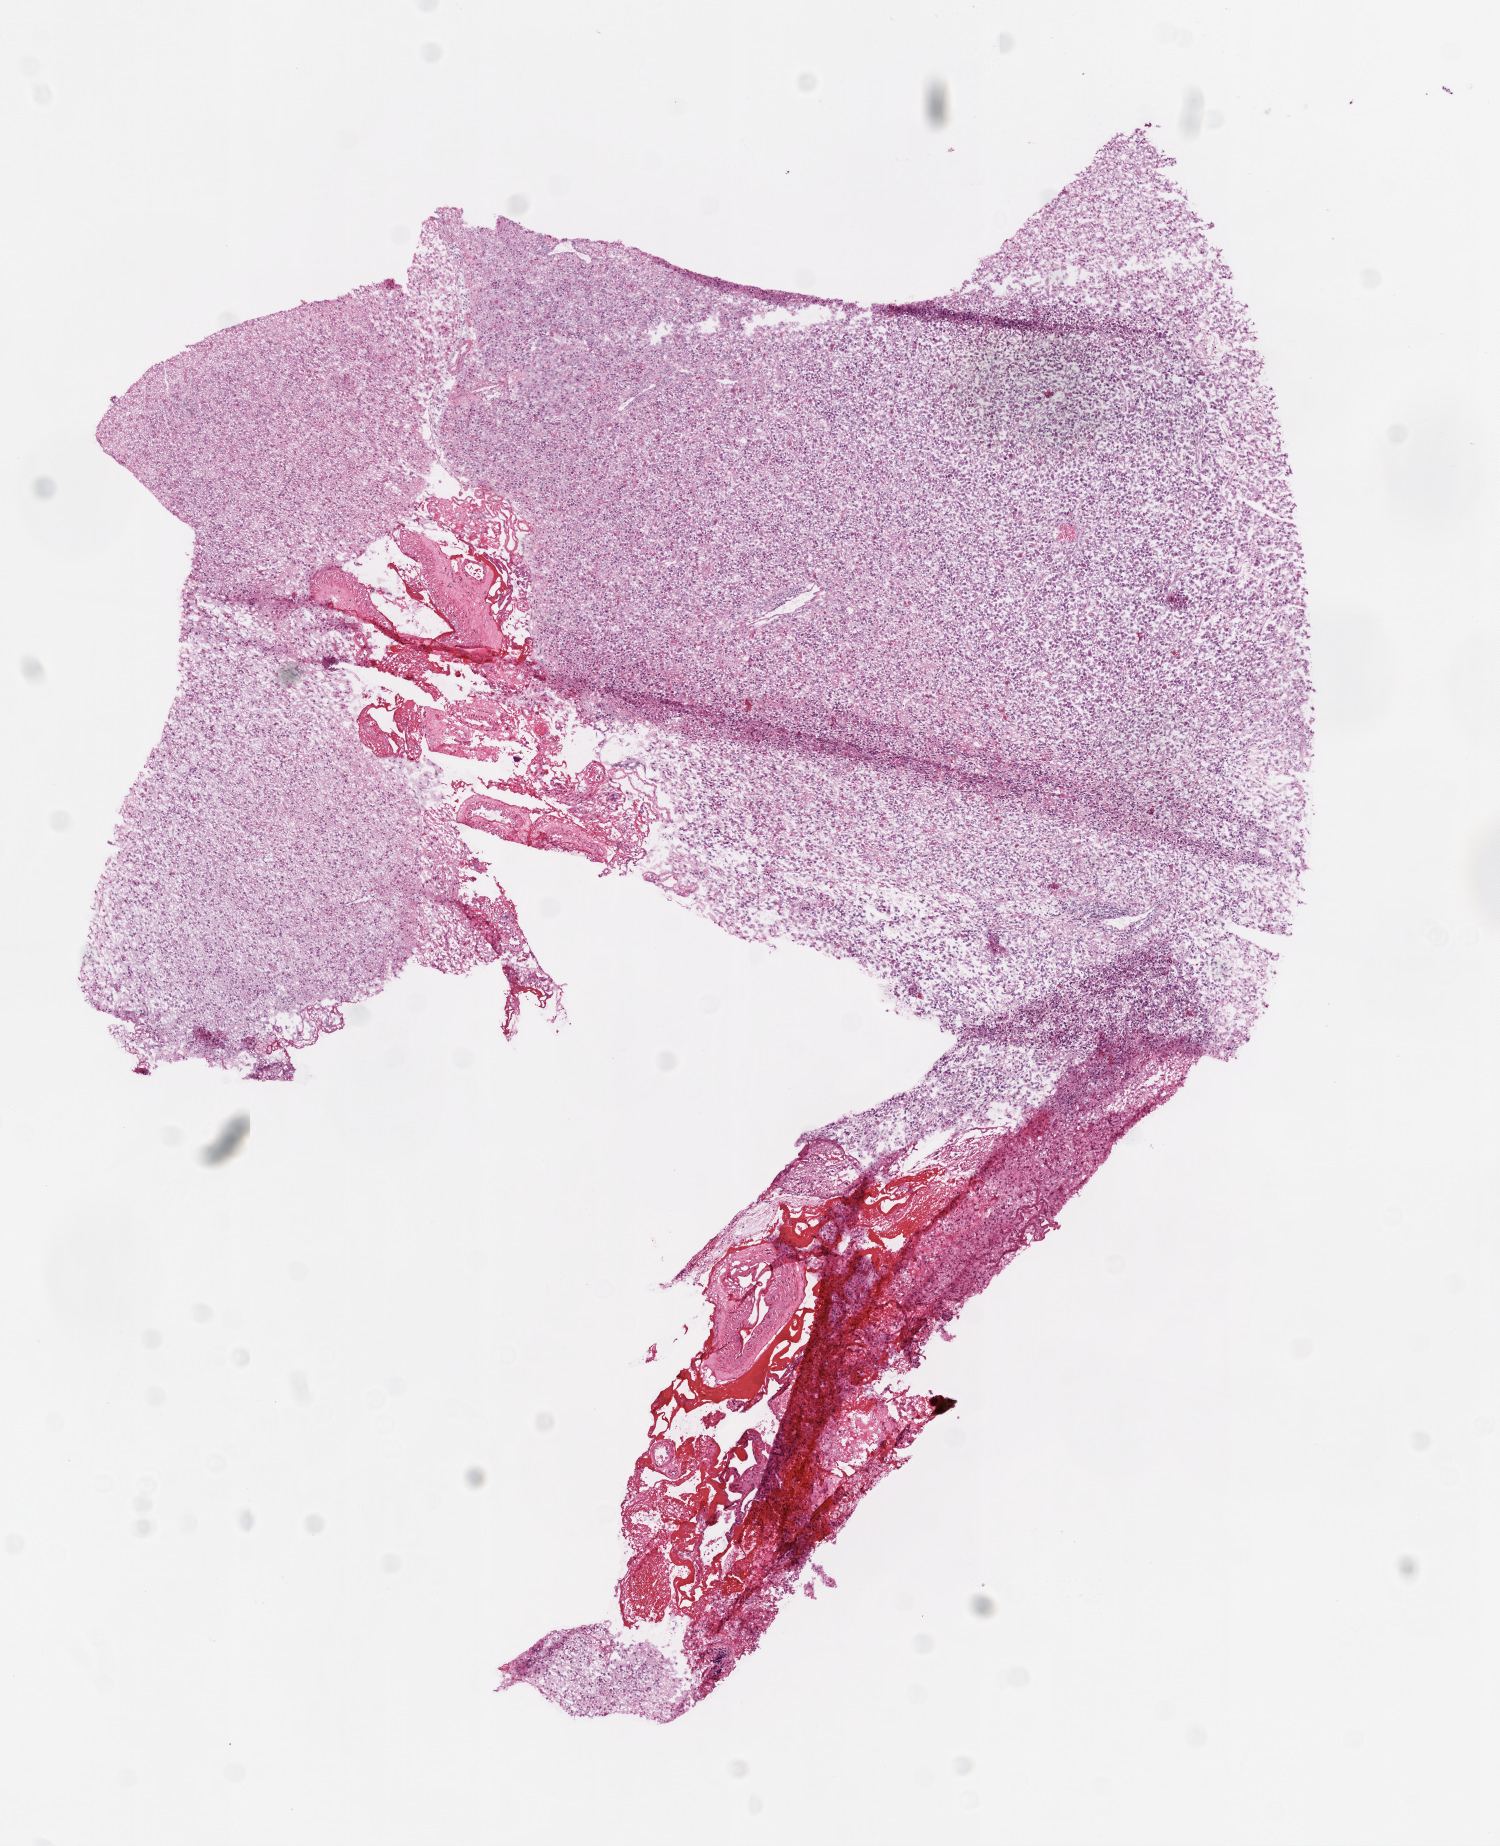
Digitized Hematoxylin and eosin (H&E) stained tissue section (whole slide) — a low-resolution overview of the entire scanned area, about 6.0 x 7.4 mm (acquisition: 20x scan); frozen section; sample: primary tumour, brain. Patient: male, age at initial diagnosis 80 years. Composition of this section per pathologist review: tumour cells 100%, tumour nuclei 85%, normal cells 0%, stromal cells 0%, necrosis 0%.
Histologic diagnosis: Glioblastoma.